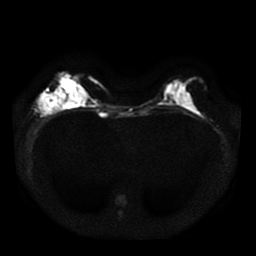
Breast MRI, one axial slice. Slice 15 of 41 in the series (ordered by position). Diffusion-weighted series; image 2 of 4 stored at this slice position (different b-values; order by instance number). 1.5 T. 256 × 256 image matrix, field of view 330 × 330 mm. Female patient.
Structures marked on this image (manually delineated by an expert):
- tumour on diffusion-weighted imaging: bounding box (x1, y1, x2, y2) in pixels: (38, 93, 62, 115)